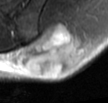
MRI of an extremity soft-tissue mass, one axial slice; position 20 of 42 along the scan axis; T2-weighted fat-saturated; MR volume resampled by the dataset authors to the PET/CT grid (not the native acquisition matrix); 108 × 103 image matrix, field of view 105 × 101 mm. Male patient. From the clinical record (not read from this slice): histological type: leiomyosarcoma; grade: intermediate; site of the primary tumour: left pelvis.
Annotated regions visible in this slice (expert contour drawn on MRI and transferred to this co-registered scan by the dataset authors):
- gross tumour volume (mass): box from (x=19, y=21) to (x=81, y=77) px